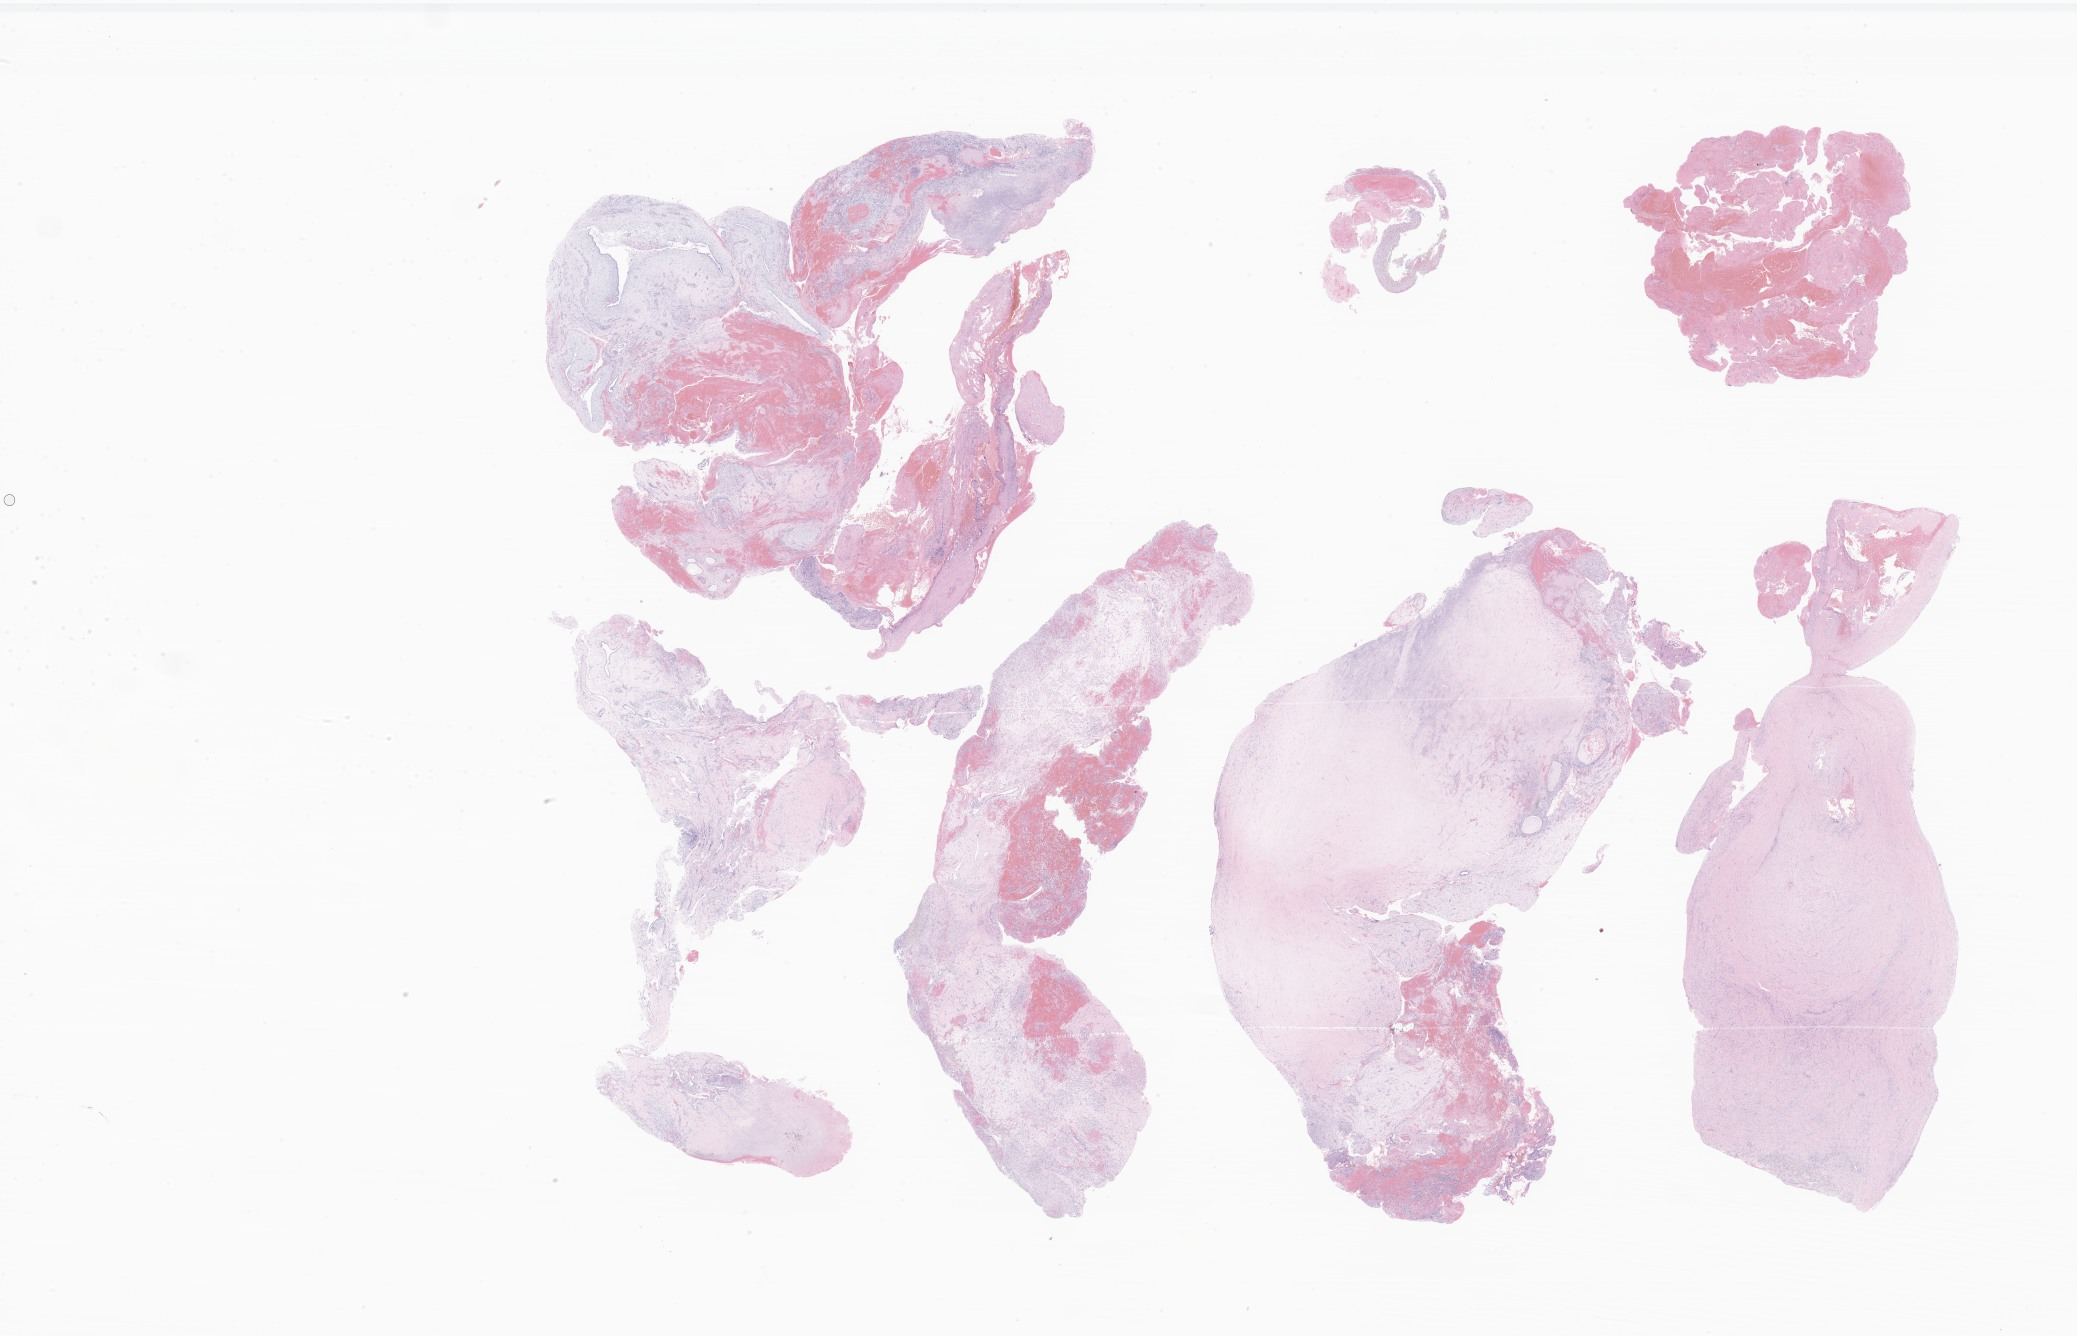
Digitized H&E-stained section of tumor tissue from the pelvis, a low-resolution overview of the entire scanned area, about 35.0 x 22.5 mm; formalin-fixed paraffin-embedded section. Patient female; age 266 months.
Diagnosis: Embryonal rhabdomyosarcoma, NOS.